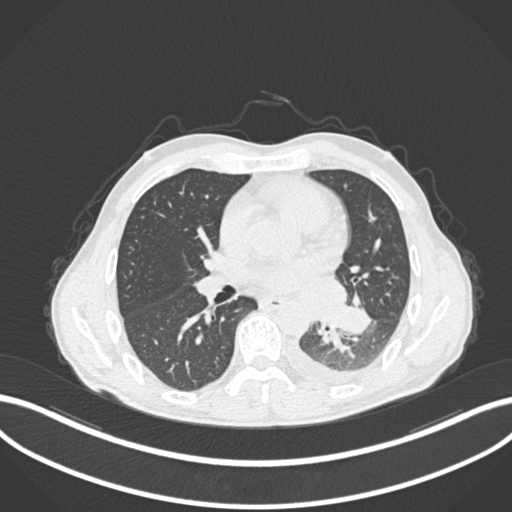
Chest CT, one axial slice; reconstruction kernel B30f; lung window (W 1500 / L -600 HU); 1 mm slice thickness; 512 × 512 image matrix. Patient: male, 47 years. Case-level facts recorded for this patient, not image findings: clinical TNM (as recorded): T3 N1 M1c; histopathological grade: G3.
Structures marked on this image (bounding box drawn by a radiologist):
- lung tumour (recorded histology: small cell carcinoma): bounding box (x1, y1, x2, y2) in pixels: (327, 300, 374, 338)